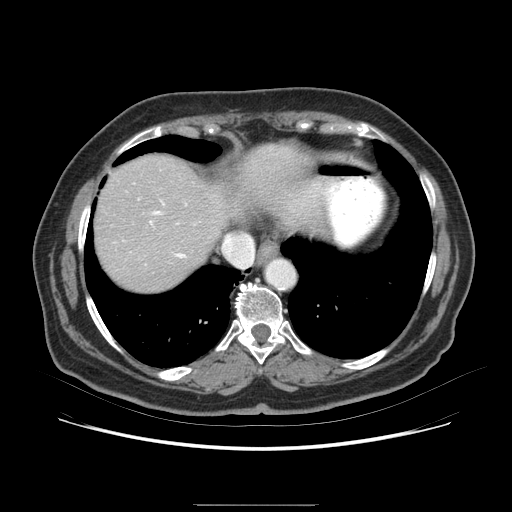
Contrast-enhanced abdominal CT (liver protocol), one axial slice. Position 69 of 79 along the scan axis. Soft-tissue window (W 400 / L 40 HU). 2.5 mm slice thickness. 512 × 512 image matrix. From the clinical record (not read from this slice): diagnosis: hepatocellular carcinoma (patient treated with transarterial chemoembolisation; whether this scan precedes or follows treatment is not stated here); TNM stage (as recorded): Stage-I; Child-Pugh class: A; tumour differentiation: poorly differentiated; tumour nodularity: uninodular.
Annotated regions visible in this slice (semi-automatically segmented with operator editing):
- liver parenchyma outside the tumour (the mass and vessels are separate outlines, so this box may not span the whole liver): box from (x=102, y=162) to (x=203, y=268) px
- liver vessels: (x=171, y=210)–(x=175, y=212)